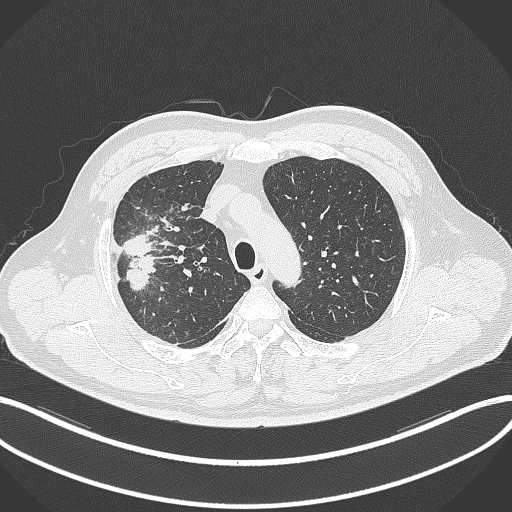
Chest CT, one axial slice; slice 261 of 348 in the series (ordered by position); 120 kVp; lung window (W 1500 / L -600 HU); 1 mm slice thickness; 512 × 512 image matrix, field of view 400 × 400 mm. Male patient, age 55 years. Case-level facts recorded for this patient, not image findings: clinical TNM (as recorded): T3 N2 M1.
Annotated regions visible in this slice (bounding box drawn by a radiologist):
- lung tumour (recorded histology: adenocarcinoma): bounding box <121,229,157,293> (left, top, right, bottom; pixels)